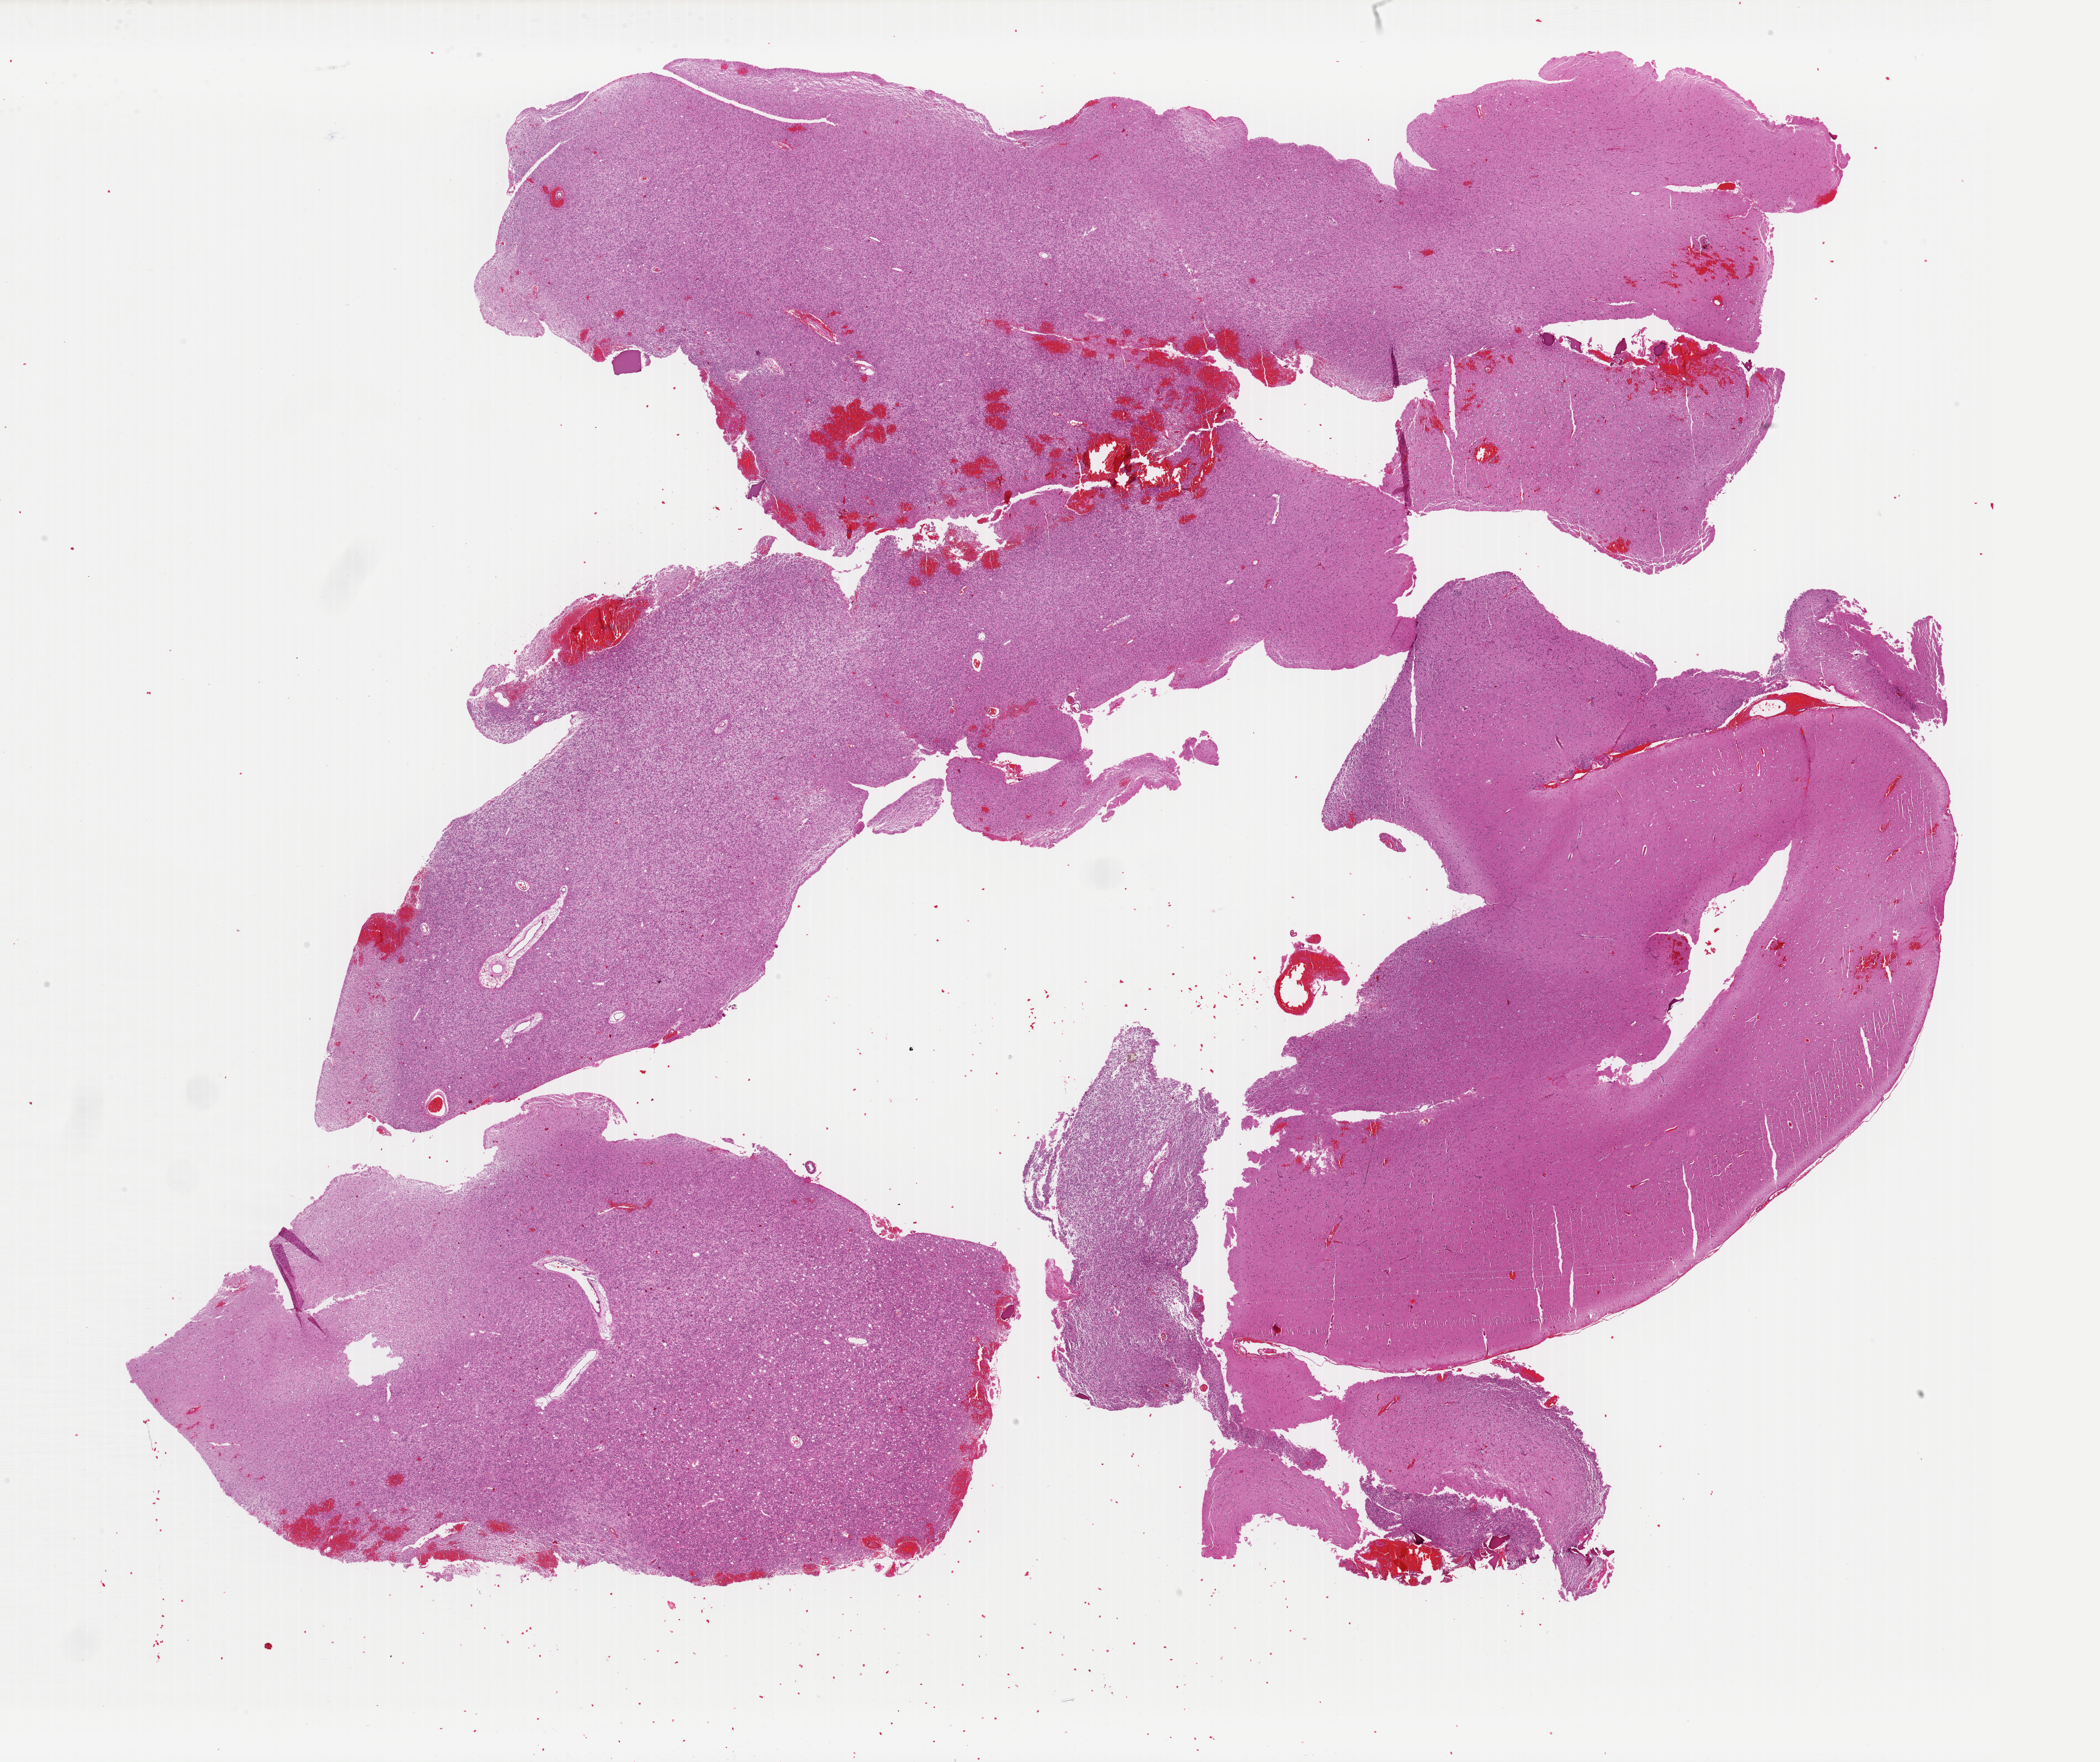
Hematoxylin and eosin (H&E) stained whole-slide image — low-resolution overview of the scanned area, about 28.0 x 23.5 mm. FFPE section. Brain, recurrent tumour sample. Patient: female, age at initial diagnosis 27 years.
This section: recurrent tumour. Patient diagnosis: Oligodendroglioma, NOS (temporal lobe).